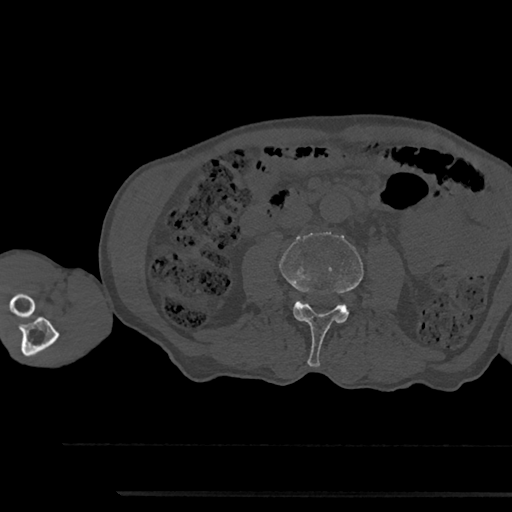
CT including the spine, one axial slice; slice 477 of 797 in the series (ordered by position); reconstruction kernel Br40s/3; 120 kVp; bone window (W 1800 / L 400 HU); 0.5 mm slice thickness; 512 × 512 image matrix. Patient: male, 79 years. From the clinical record (not read from this slice): primary cancer: prostate.
Annotated regions visible in this slice (semi-automatically segmented with operator editing):
- L3 vertebra: bounding box (x1, y1, x2, y2) in pixels: (279, 232, 363, 367)